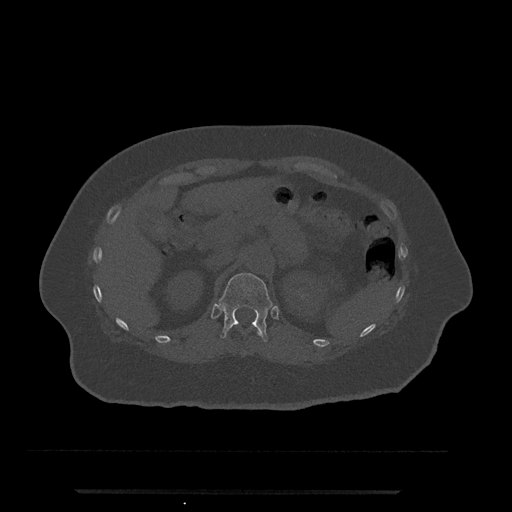
CT including the spine, one axial slice. Position 183 of 797 along the scan axis. Reconstruction kernel Br40s/3. Bone window (W 1800 / L 400 HU). 0.5 mm slice thickness. 512 × 512 image matrix, field of view 440 × 440 mm. Female patient, age 51 years. Case-level facts recorded for this patient, not image findings: primary cancer: neuro.
Outlined on this slice (semi-automatic segmentation, software-assisted and operator-edited):
- T11 vertebra: bounding box [x1, y1, x2, y2] px = [241, 330, 261, 354]
- T12 vertebra: [218, 273, 273, 342]